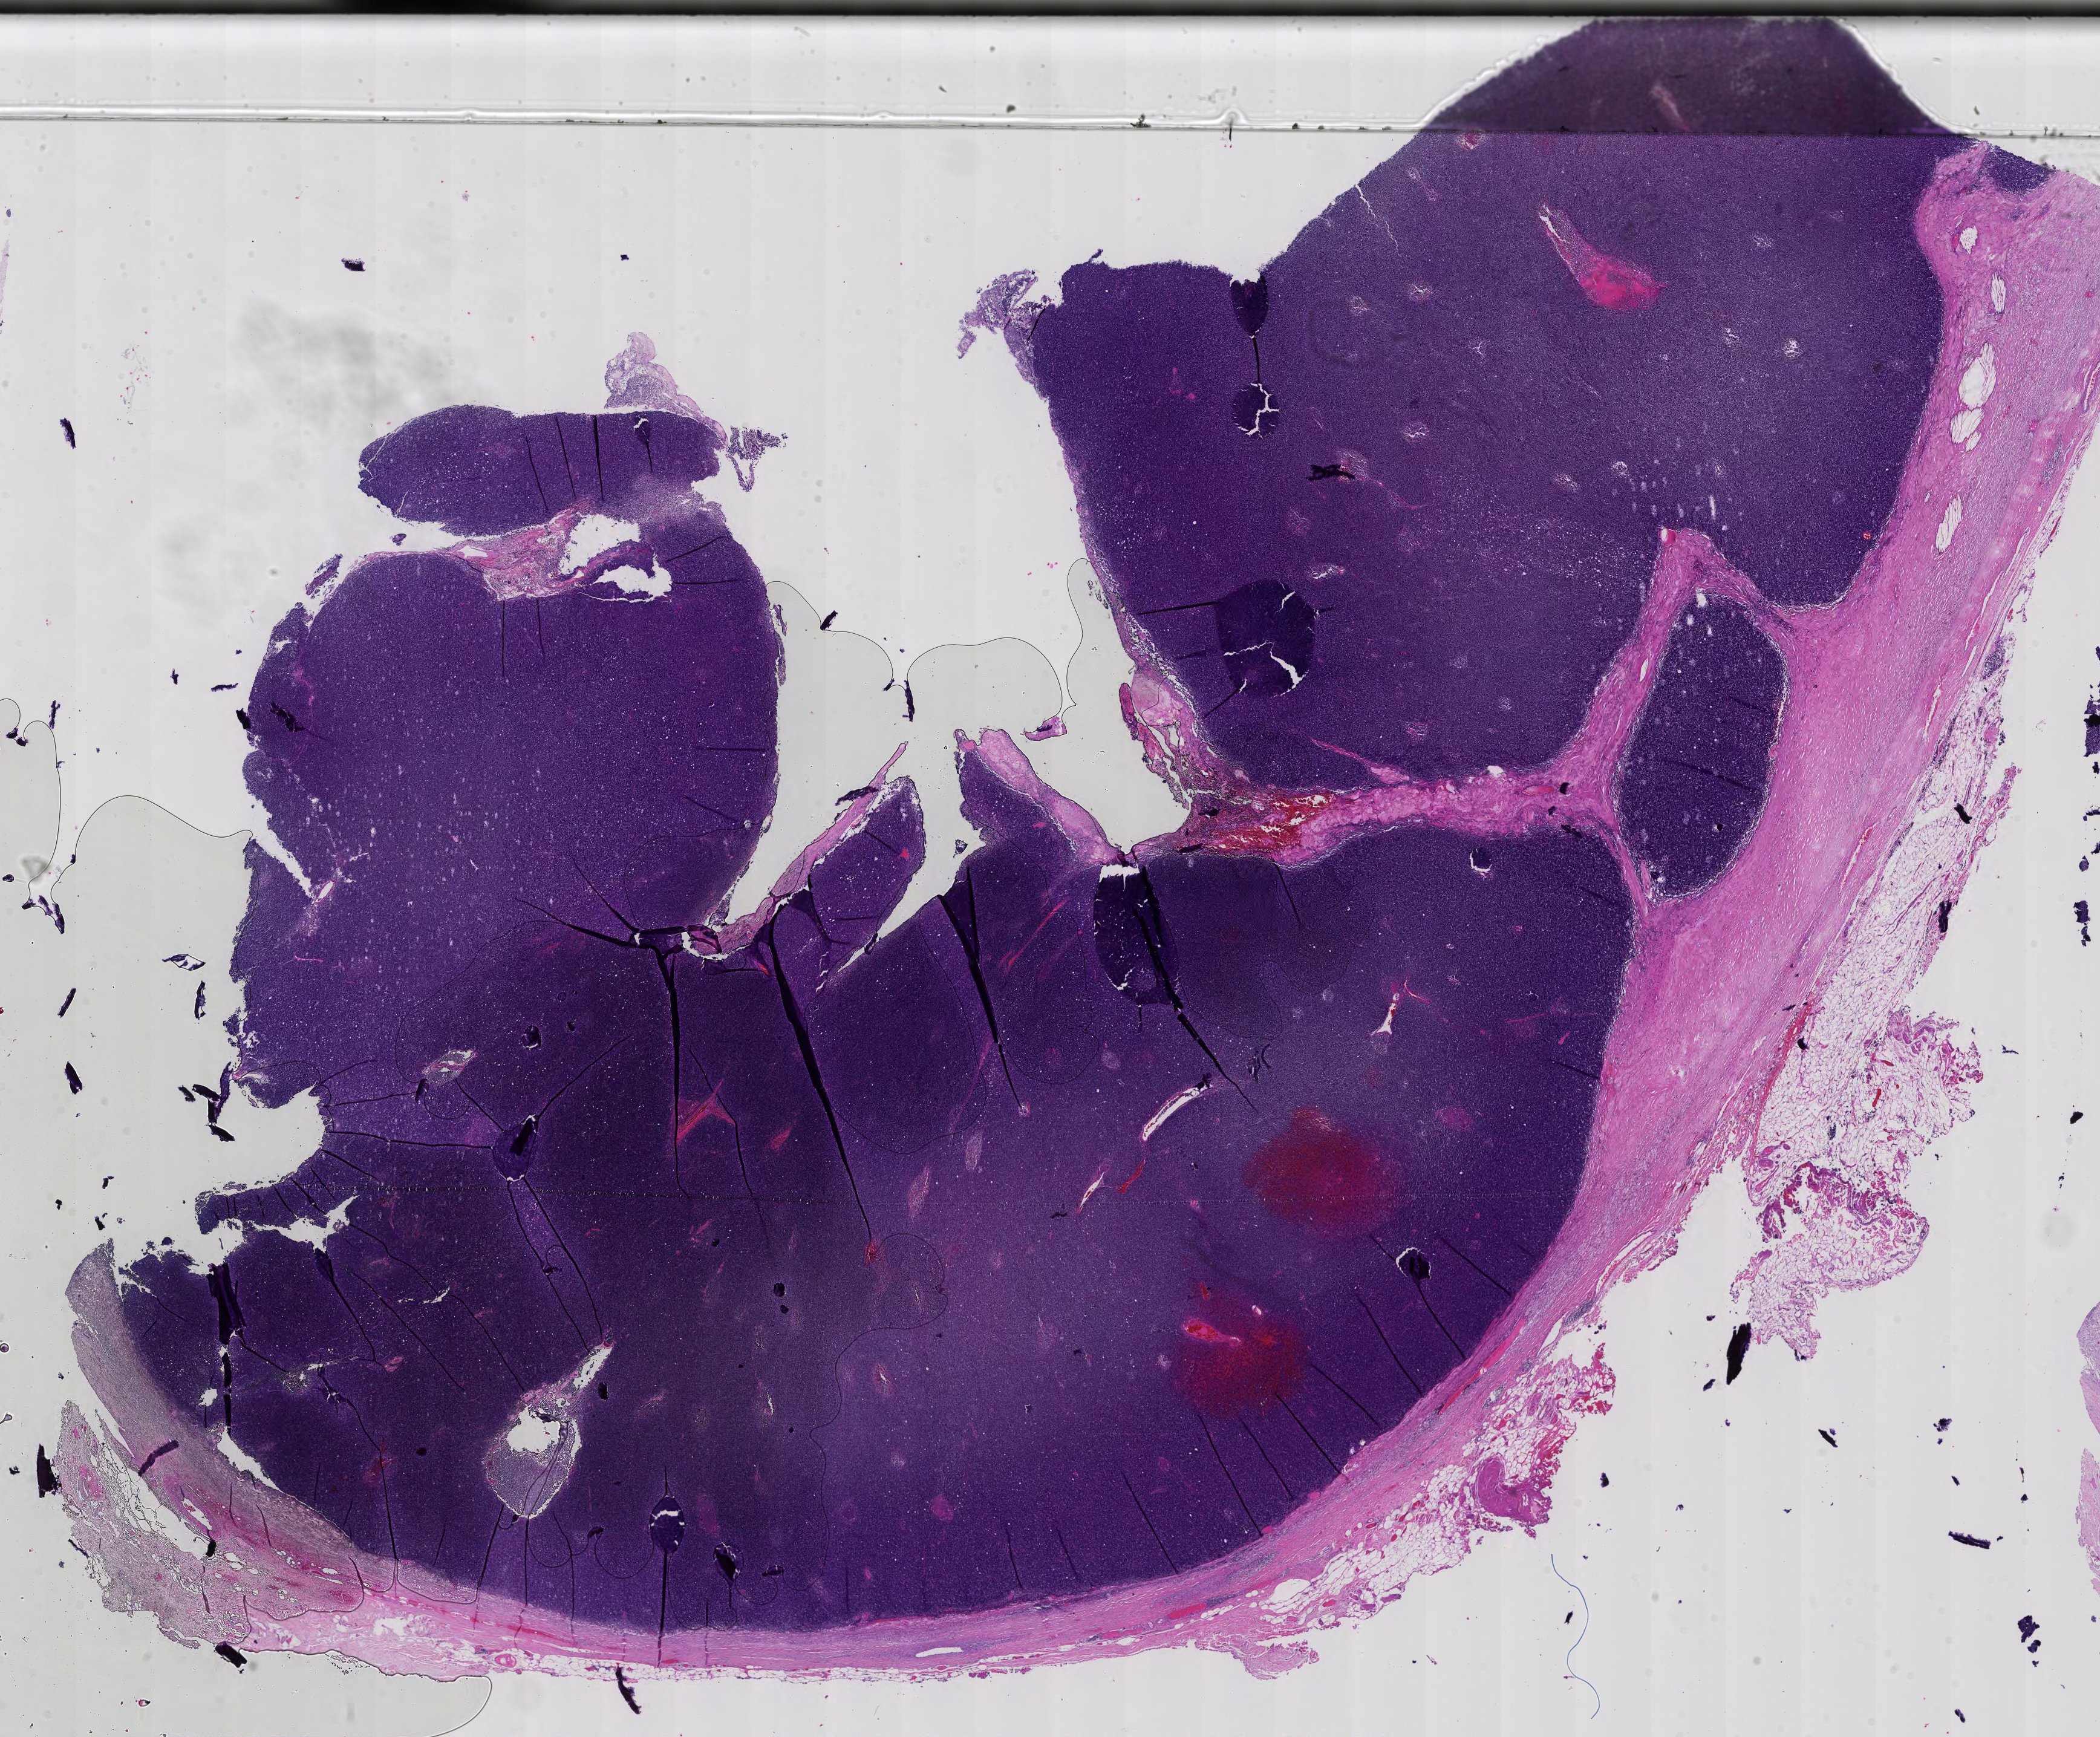
H&E-stained whole-slide image — whole scanned area (about 25.3 x 20.9 mm, acquisition: 40x scan) shown as a low-resolution overview; formalin-fixed paraffin-embedded (FFPE) diagnostic section; primary tumour sample from the thymus. Male, age 73 years at initial diagnosis.
Diagnosis: Thymoma, type B1, malignant (anterior mediastinum).